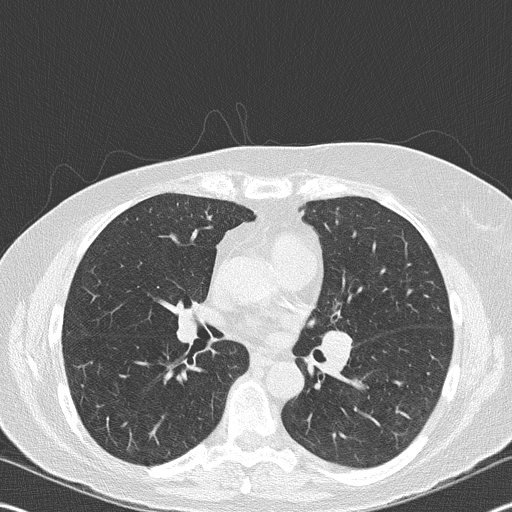
Low-dose screening chest CT, one axial slice. Position 96 of 177 along the scan axis. Reconstruction kernel B50f. 120 kVp. Lung window (W 1500 / L -600 HU). 512 × 512 image matrix, field of view 342 × 342 mm.
Outlined on this slice (outlined manually by an expert reader):
- lesion 2 (nodule, hilum of left lung): bounding box [x1, y1, x2, y2] px = [323, 329, 352, 371]